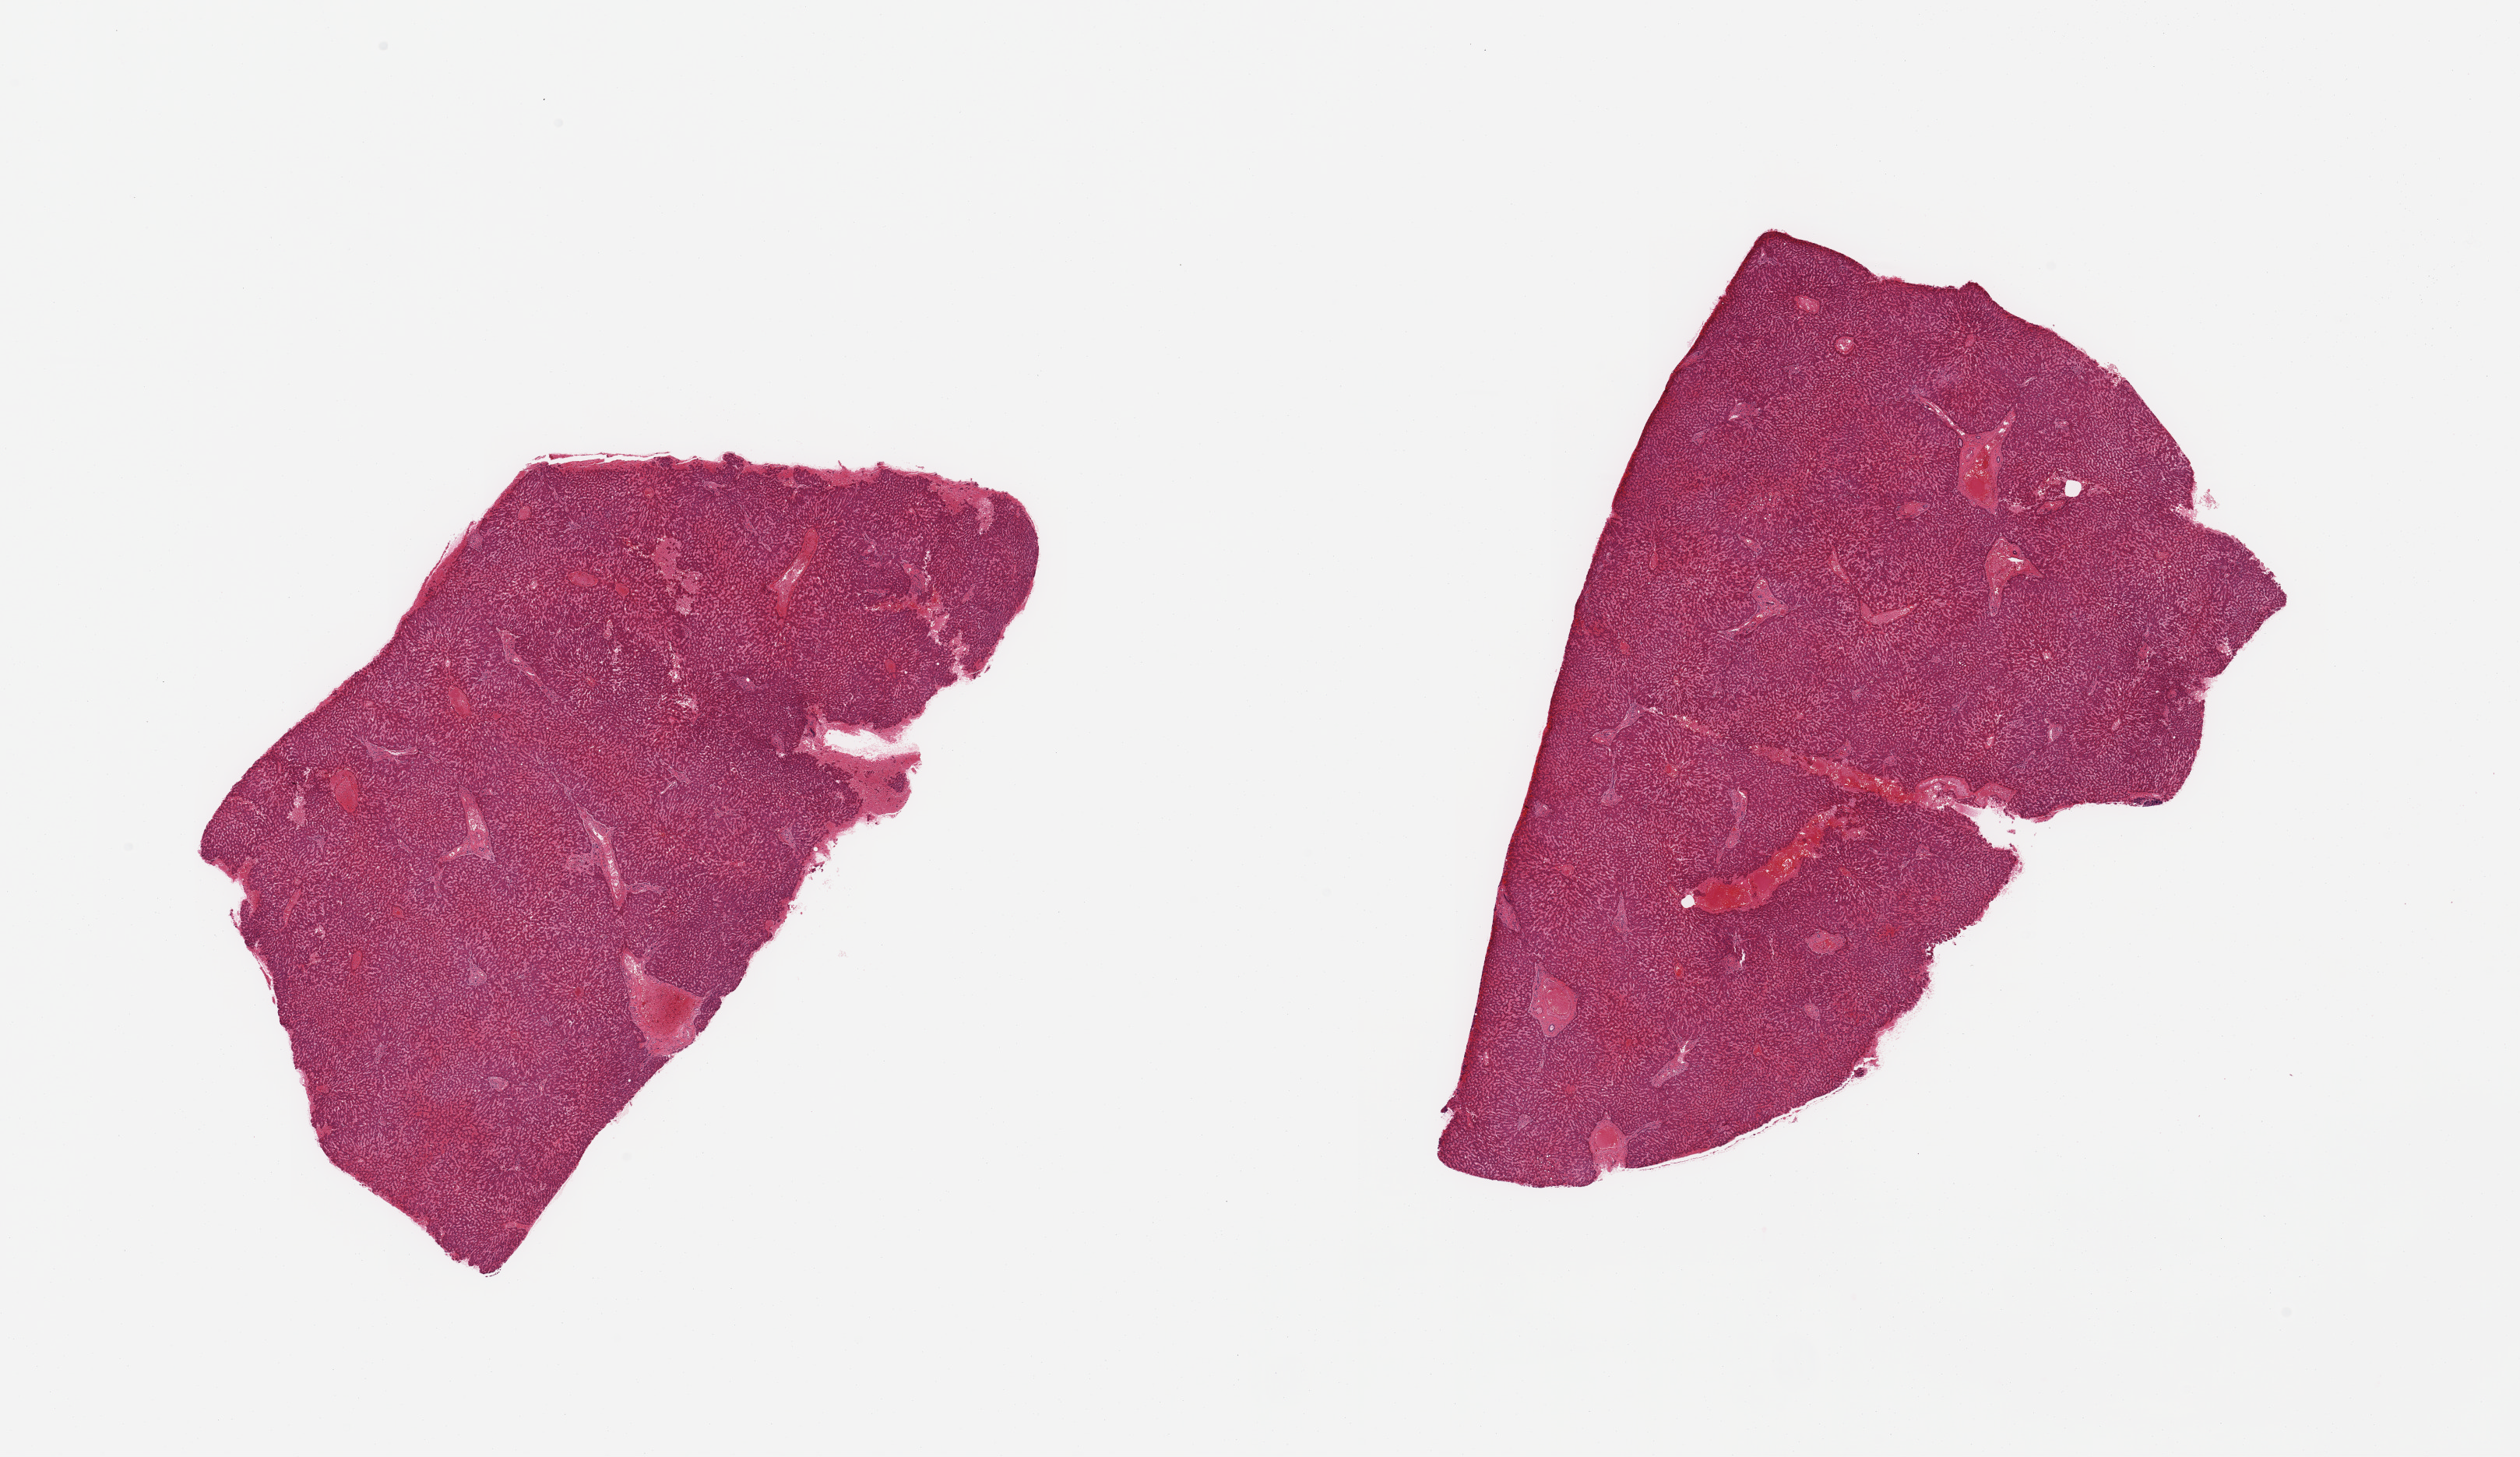
Whole-slide image, haematoxylin and eosin stain — whole scanned area (about 25.6 x 14.8 mm) shown as a low-resolution overview. PAXgene-fixed, paraffin-embedded tissue. Target tissue: liver. Donor tissue sample. Donor: male.
Reviewer comment on this tissue sample: 2 pieces; no active or chronic lesions.